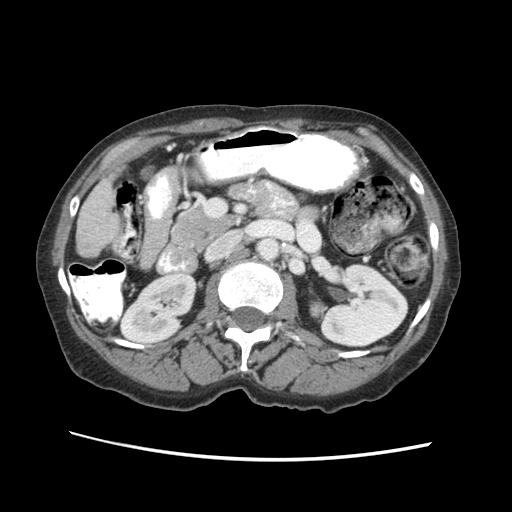
Contrast-enhanced abdominal CT (liver protocol), one axial slice; position 11 of 63 along the scan axis; soft-tissue window (W 400 / L 40 HU); 2.5 mm slice thickness; 512 × 512 image matrix, field of view 340 × 340 mm. From the clinical record (not read from this slice): diagnosis: hepatocellular carcinoma (patient treated with transarterial chemoembolisation; whether this scan precedes or follows treatment is not stated here); TNM stage (as recorded): Stage-I; Child-Pugh class: B; tumour differentiation: well differentiated; tumour nodularity: uninodular.
Outlined on this slice (semi-automatic segmentation, software-assisted and operator-edited):
- liver parenchyma outside the tumour (the mass and vessels are separate outlines, so this box may not span the whole liver): bounding box (x1, y1, x2, y2) in pixels: (78, 178, 118, 255)